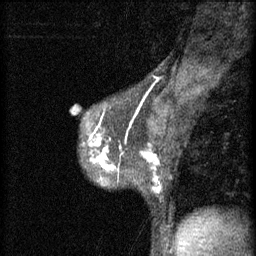
Breast MRI (dynamic contrast-enhanced), one sagittal slice; position 39 of 60 along the scan axis; 3 images stored at this slice position (order not interpretable as contrast timing); 1.5 T; TE 4.2 ms, TR 11 ms; 2 mm slice thickness; 256 × 256 image matrix. Female patient, age 37 years.
Outlined on this slice (semi-automatically segmented with operator editing):
- analysis volume of interest (the breast-tissue region the enhancement analysis was run in; not a lesion): box from (x=84, y=138) to (x=162, y=193) px
- tumour enhancement mask (voxels above the 70 % enhancement threshold inside the analysis volume of interest): (x=89, y=138)–(x=160, y=193)